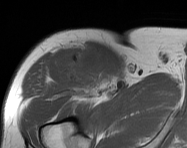
MRI of an extremity soft-tissue mass, one axial slice. MR volume resampled by the dataset authors to the PET/CT grid (not the native acquisition matrix). 3.27 mm slice thickness. 187 × 148 image matrix, field of view 183 × 145 mm. Male patient. Case-level facts recorded for this patient, not image findings: histological type: pleiomorphic leiomyosarcoma; grade: intermediate; site of the primary tumour: right thigh.
Annotated regions visible in this slice (expert contour drawn on MRI and transferred to this co-registered scan by the dataset authors):
- gross tumour volume including surrounding oedema: bounding box <66,45,112,92> (left, top, right, bottom; pixels)
- gross tumour volume (mass): <73,54,110,91>